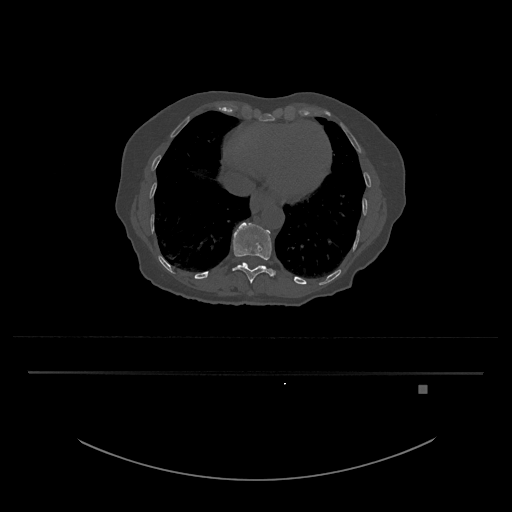
CT including the spine, one axial slice; position 661 of 797 along the scan axis; reconstruction kernel Br40s/3; bone window (W 1800 / L 400 HU); 0.5 mm slice thickness; 512 × 512 image matrix, field of view 500 × 500 mm. Patient: female, 57 years. From the clinical record (not read from this slice): primary cancer: cervical.
Outlined on this slice (semi-automatic segmentation, software-assisted and operator-edited):
- T11 vertebra: bounding box <232,222,275,284> (left, top, right, bottom; pixels)
- T12 vertebra: <238,262,266,267>